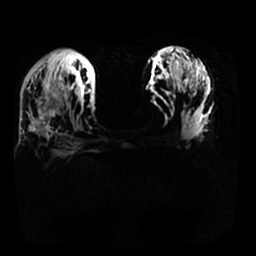
Breast MRI, one axial slice; slice 15 of 25 in the series (ordered by position); diffusion-weighted series; image 2 of 4 stored at this slice position (different b-values; order by instance number); 1.5 T; 4 mm slice thickness; 256 × 256 image matrix, field of view 340 × 340 mm. Female patient.
Annotated regions visible in this slice (manually delineated by an expert):
- tumour on diffusion-weighted imaging: bounding box [x1, y1, x2, y2] px = [35, 83, 60, 129]